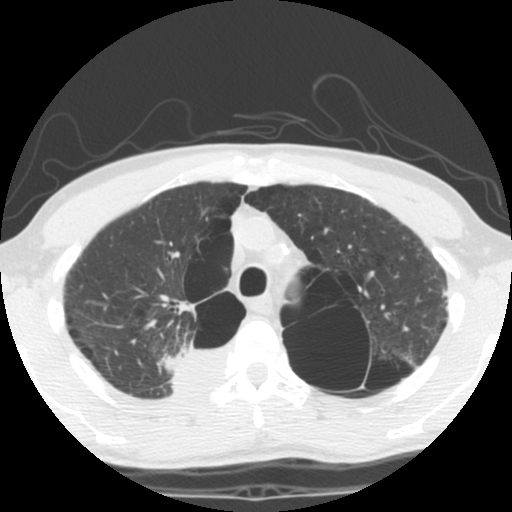
Low-dose screening chest CT, one axial slice; position 88 of 119 along the scan axis; reconstruction kernel STANDARD; lung window (W 1500 / L -600 HU); 512 × 512 image matrix, field of view 295 × 295 mm.
Outlined on this slice (manually delineated by an expert):
- lesion 1 (tumor, upper lobe of right lung): box from (x=166, y=347) to (x=229, y=393) px